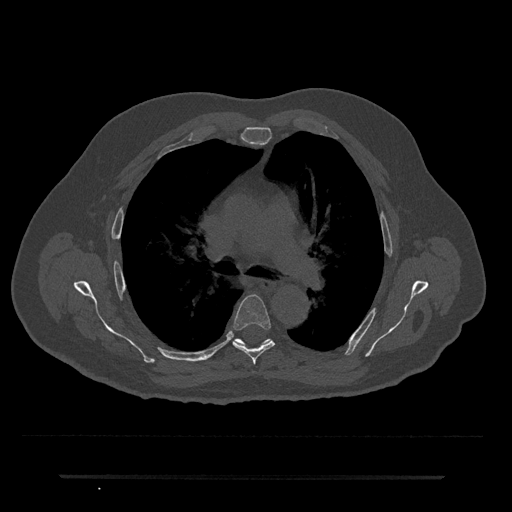
CT including the spine, one axial slice. Reconstruction kernel Br40s/3. 120 kVp. Bone window (W 1800 / L 400 HU). 0.5 mm slice thickness. 512 × 512 image matrix. Male patient, age 69 years. Case-level facts recorded for this patient, not image findings: primary cancer: prostate.
Structures marked on this image (semi-automatic segmentation, software-assisted and operator-edited):
- T5 vertebra: bounding box (x1, y1, x2, y2) in pixels: (233, 295, 275, 364)
- T6 vertebra: (236, 339, 241, 343)